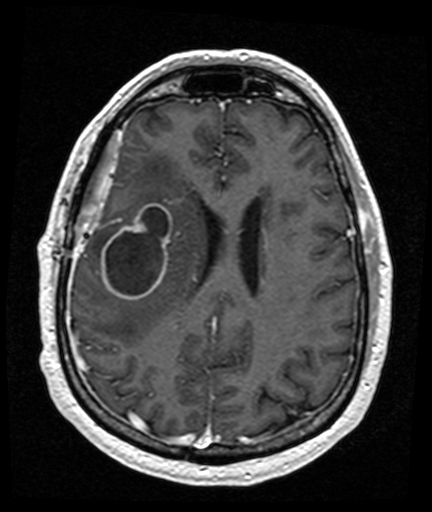
Brain MRI from a brain-tumour surgery series, one axial slice. Position 60 of 176 along the scan axis. T1-weighted post-contrast. 432 × 512 image matrix, field of view 194 × 230 mm. Case-level facts recorded for this patient, not image findings: histopathology: Glioblastoma; WHO grade: 4; IDH mutation: no.
Outlined on this slice (outlined manually by an expert reader):
- tumour: bounding box (x1, y1, x2, y2) in pixels: (102, 204, 173, 300)